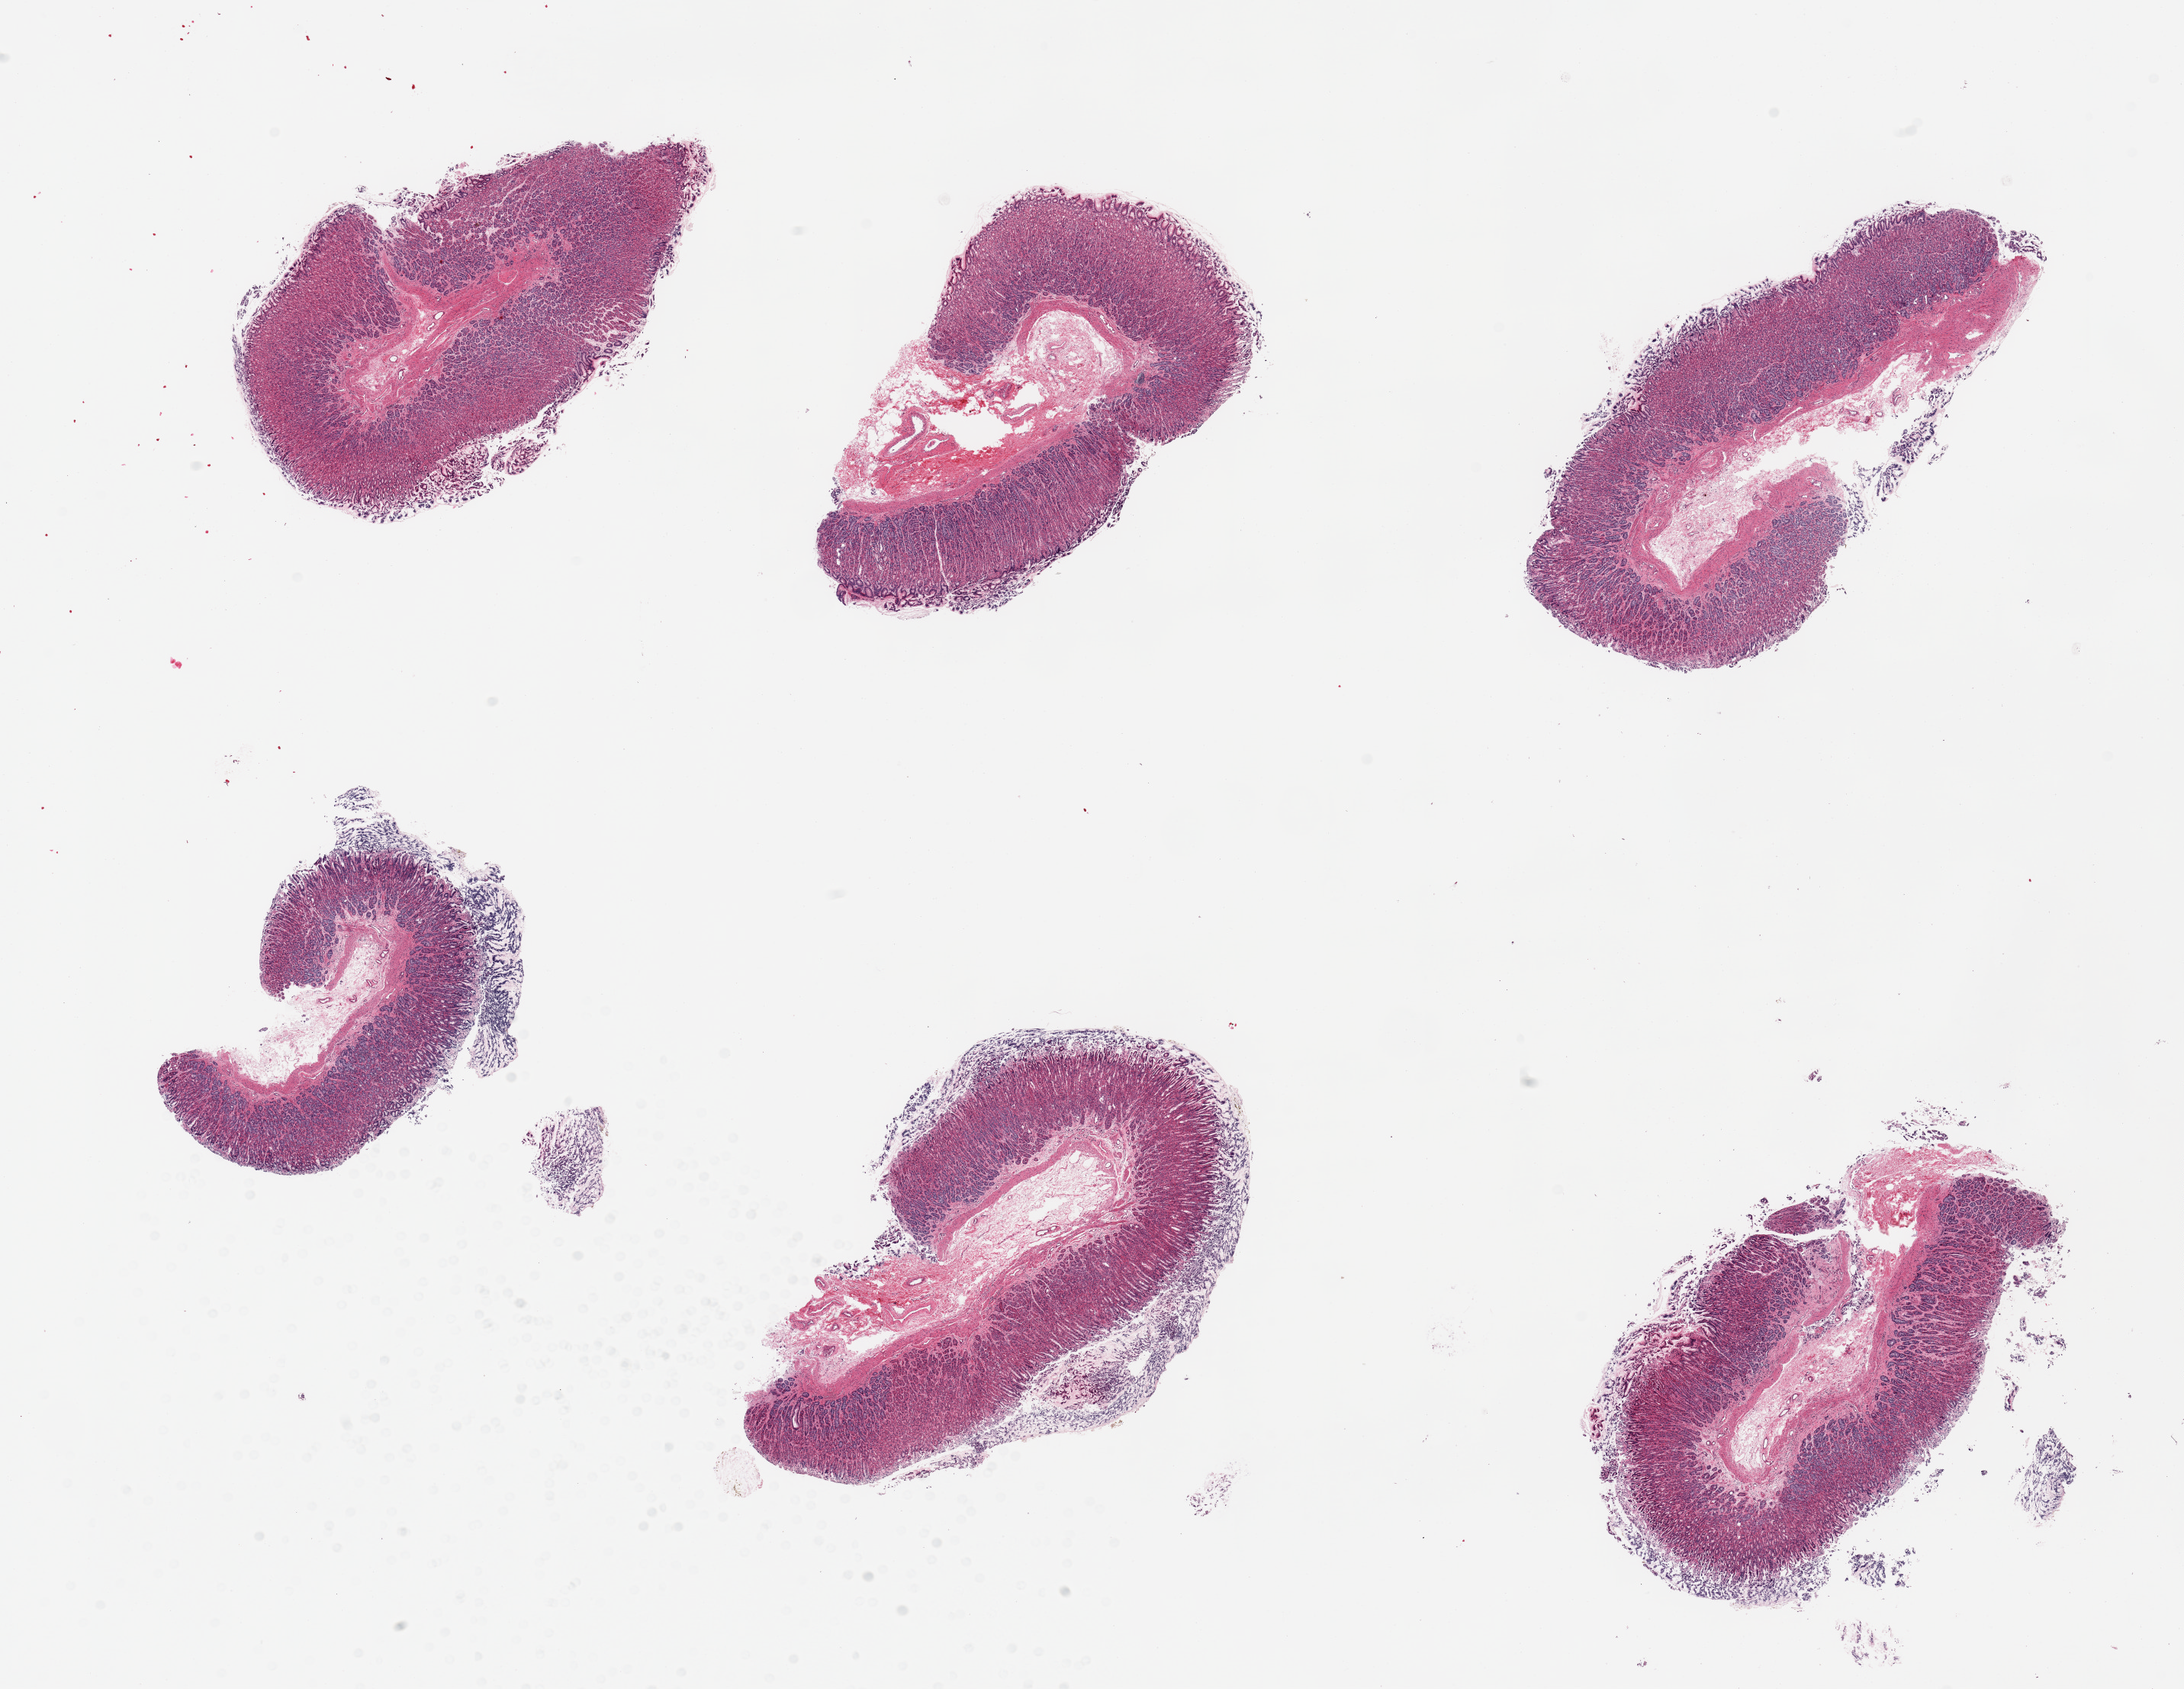
Digitized hematoxylin and eosin (H&E)-stained section, brightfield, low-resolution overview of the scanned area, about 22.6 x 17.5 mm. PAXgene-fixed, paraffin-embedded tissue. Sampled site (target tissue): stomach. Donor tissue sample. Male donor.
* pathologist's review note for this sample: 6 pieces, excellent speicmen,well preserved mucosa up to 1mm thick, ~70% thickness